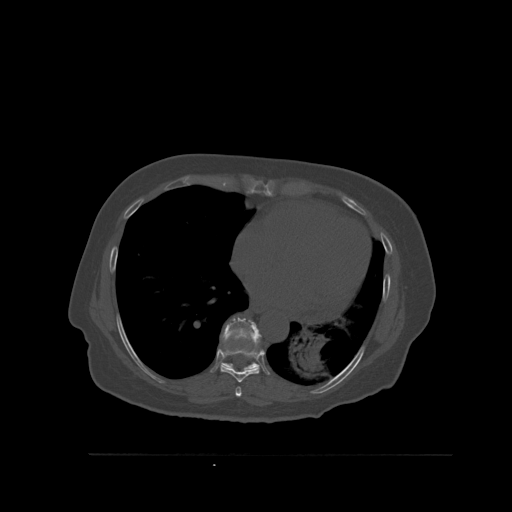
CT including the spine, one axial slice; position 346 of 527 along the scan axis; bone window (W 1800 / L 400 HU); 1.5 mm slice thickness; 512 × 512 image matrix. Female patient, age 73 years. Case-level facts recorded for this patient, not image findings: primary cancer: breast; vertebrae with lytic lesions (as recorded): L2.
Outlined on this slice (semi-automatically segmented with operator editing):
- T7 vertebra: bounding box (x1, y1, x2, y2) in pixels: (235, 387, 242, 397)
- T8 vertebra: (220, 348, 260, 383)
- T9 vertebra: (221, 318, 262, 372)